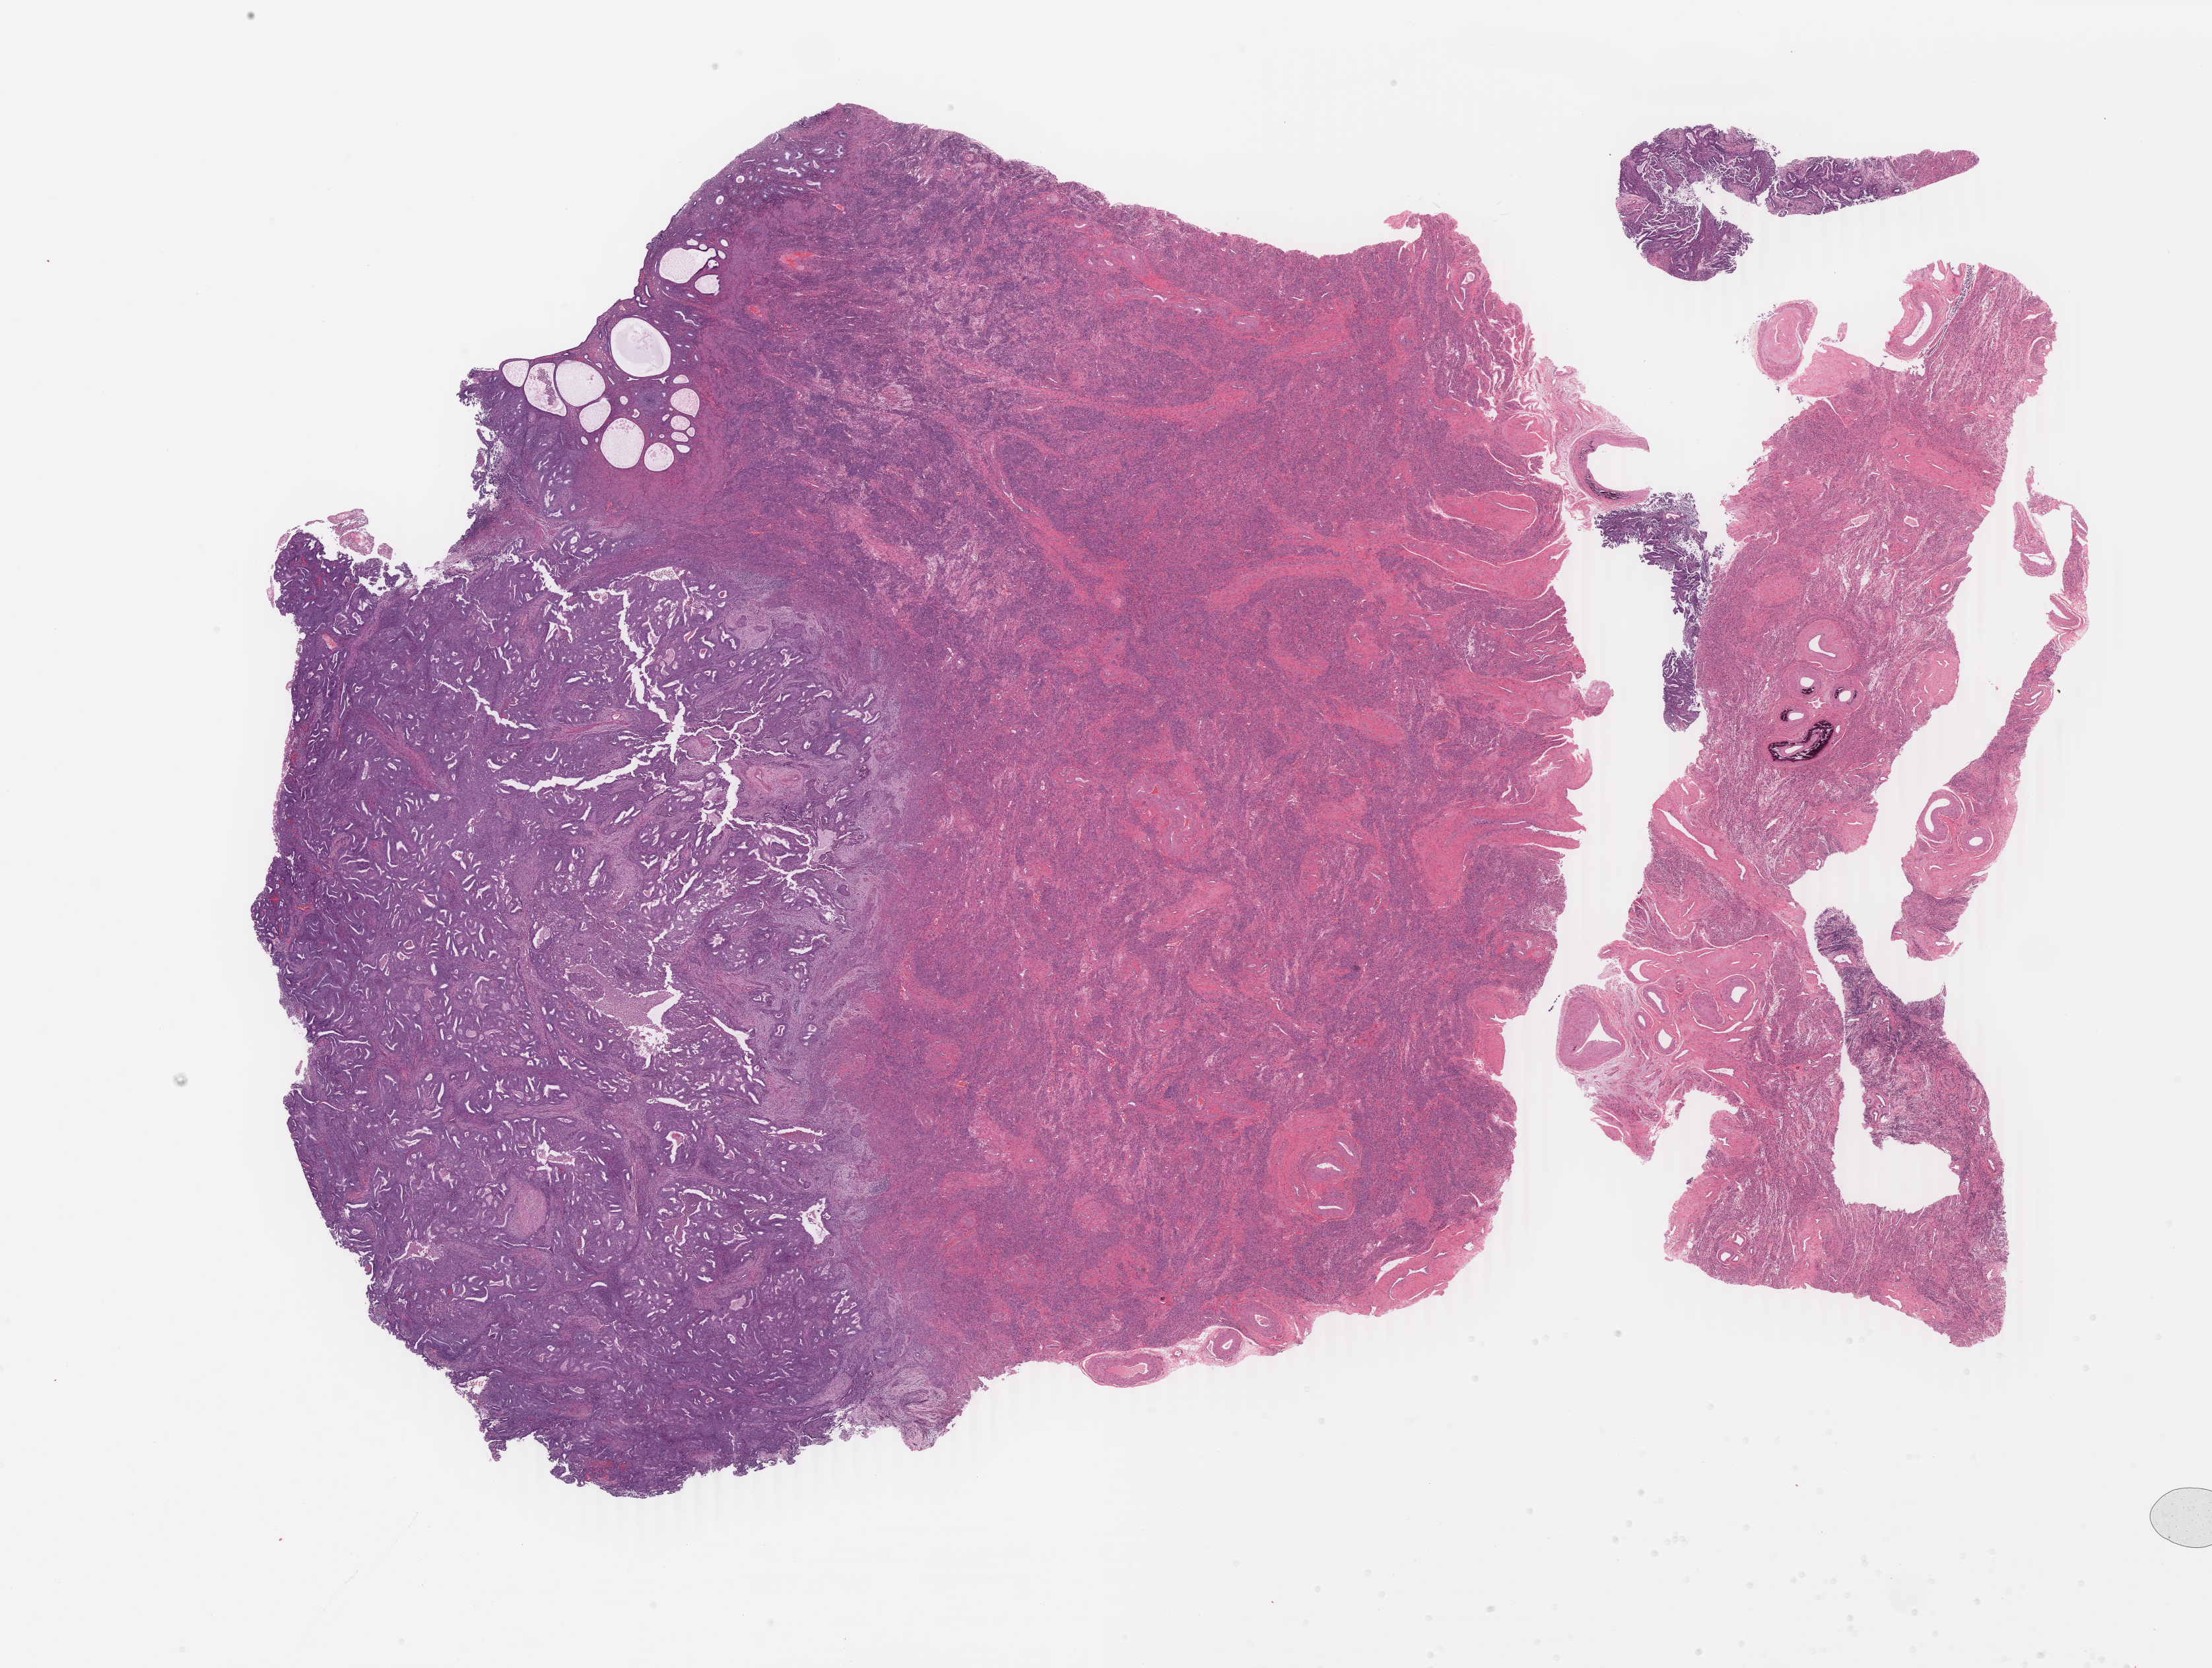
Hematoxylin and eosin (H&E) stained whole-slide image, a low-resolution overview of the entire scanned area, about 26.7 x 20.1 mm (acquisition: 40x scan). FFPE section. Sample: primary tumour, uterus. Patient: female, age at initial diagnosis 78 years. Histologic grade: G1 (well differentiated).
* FIGO stage: IA
* pathologic diagnosis: Endometrioid adenocarcinoma, NOS (endometrium)